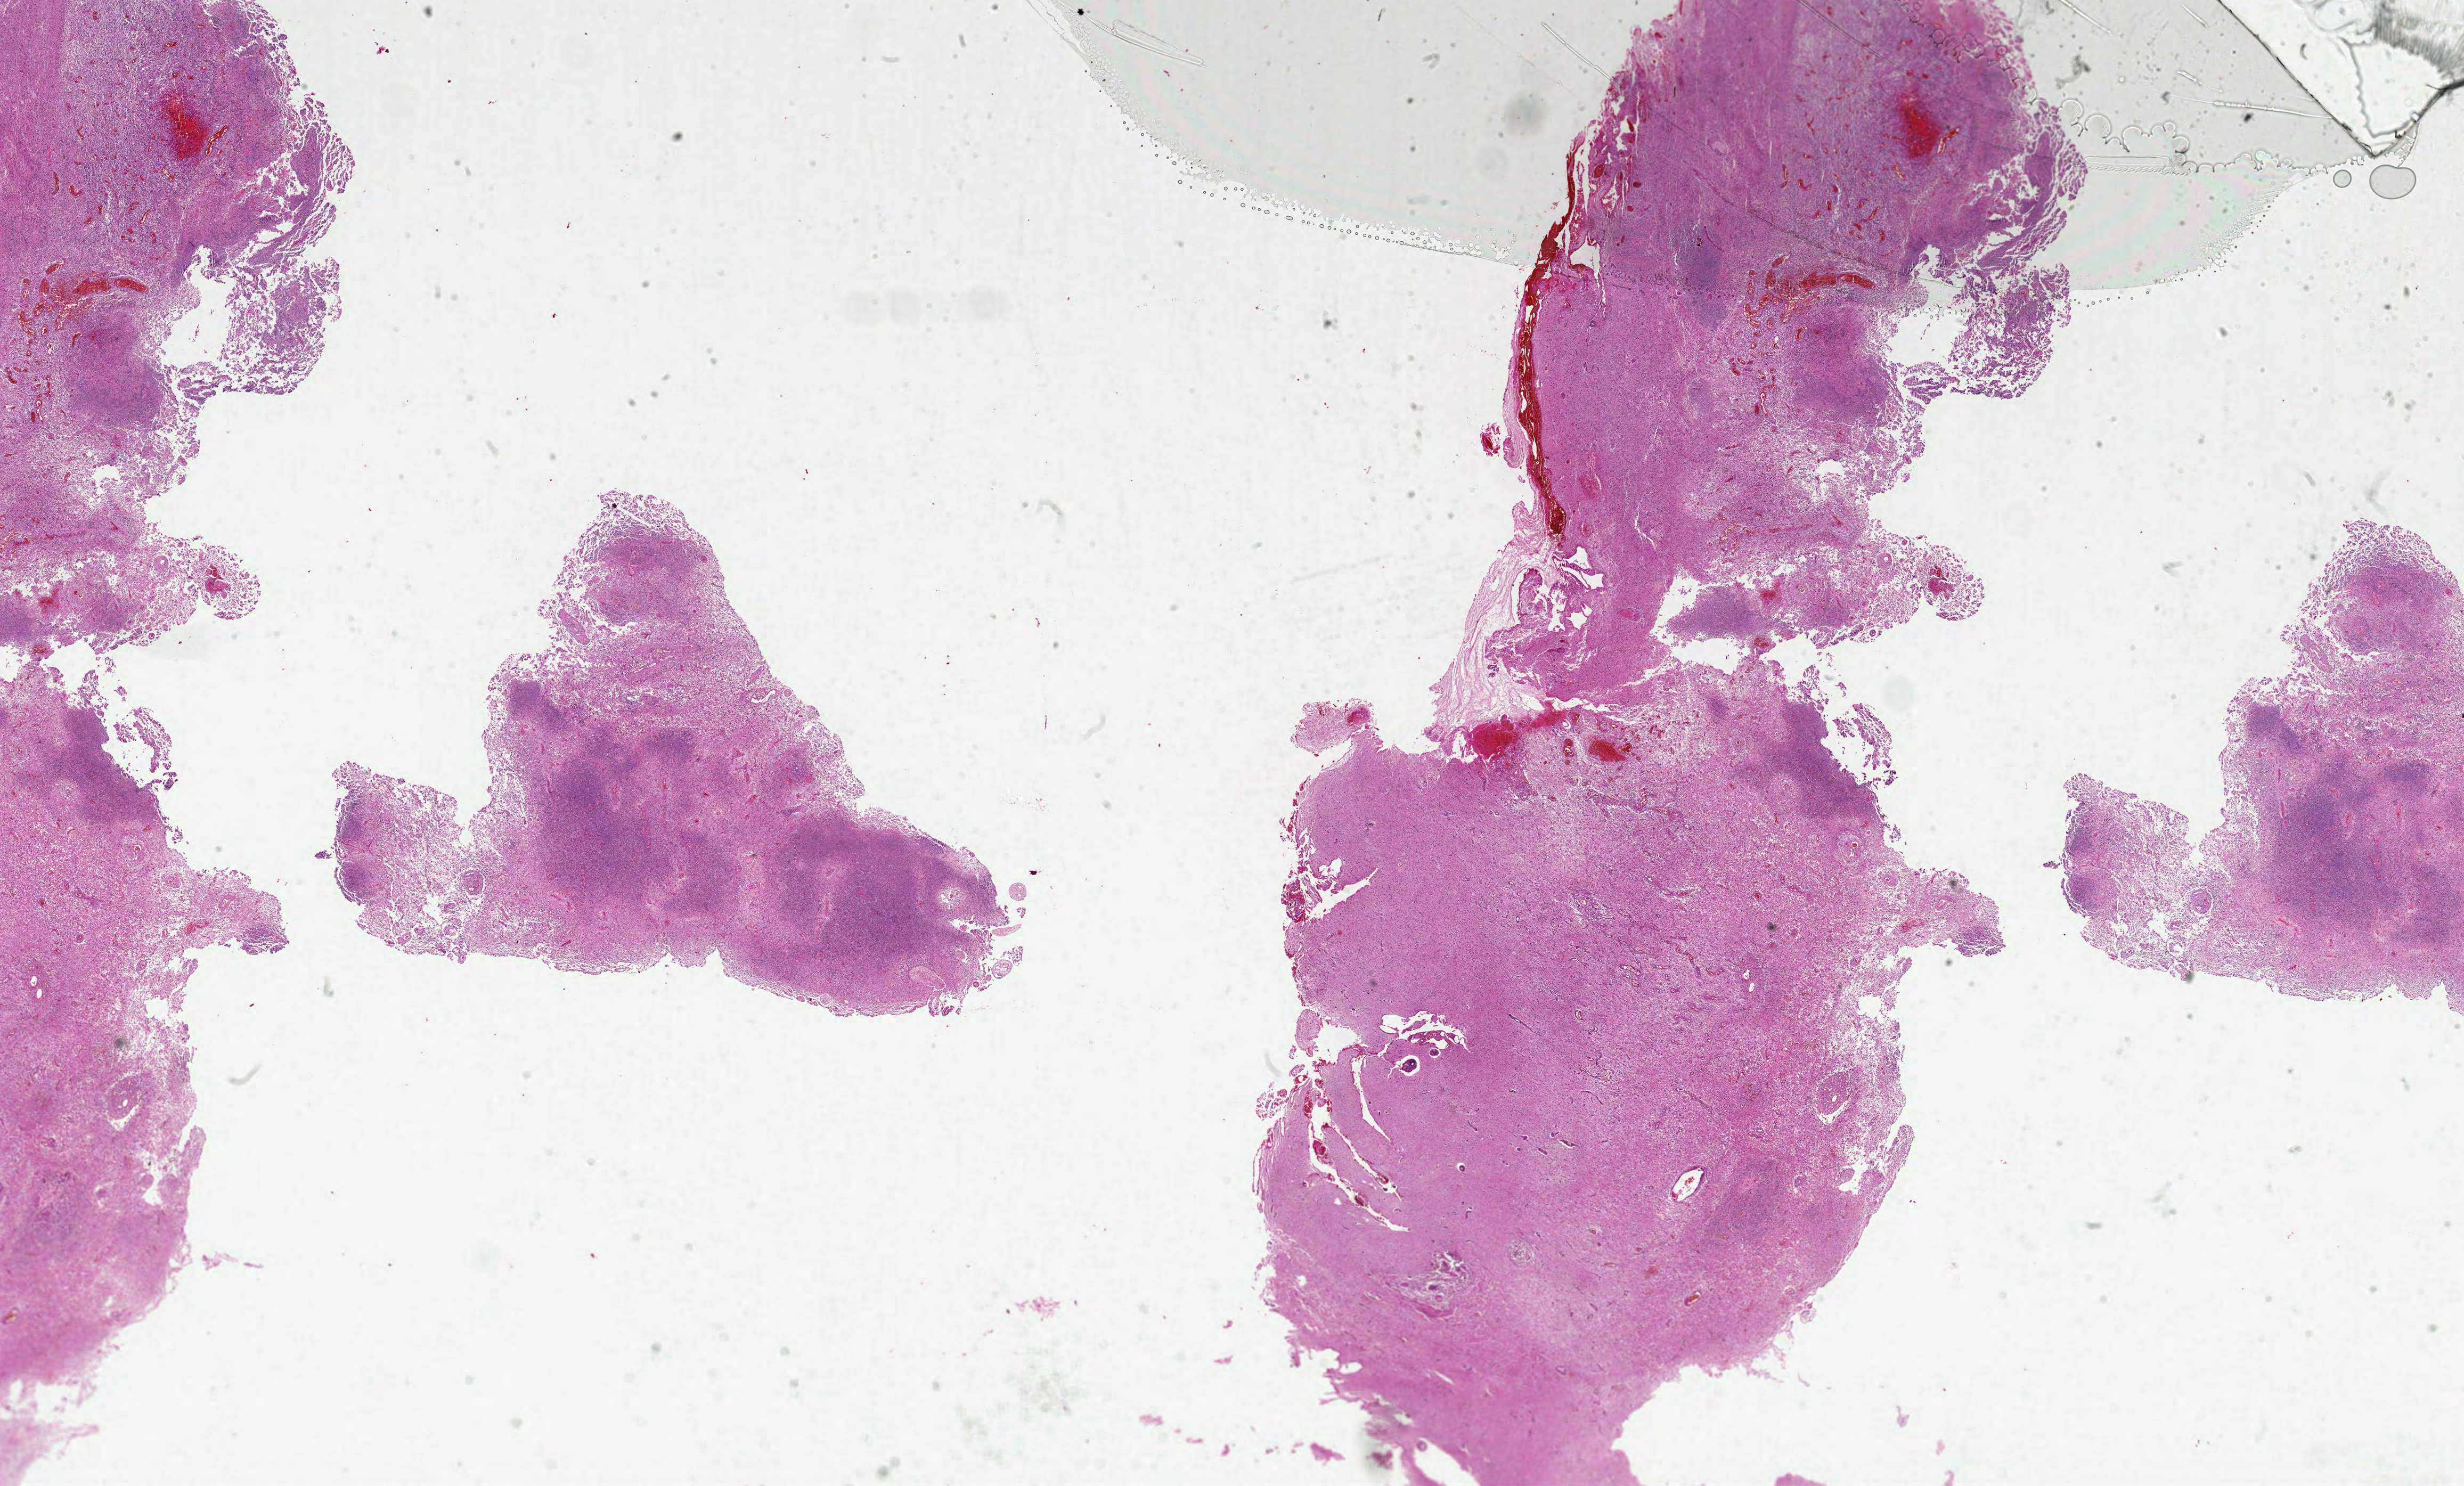
Digitized H&E-stained tissue section (whole slide) — whole scanned area (about 37.0 x 22.3 mm) shown as a low-resolution overview; formalin-fixed paraffin-embedded (FFPE) diagnostic section; brain, primary tumour sample. Patient: female, age at initial diagnosis 75 years.
* pathologic diagnosis: Glioblastoma